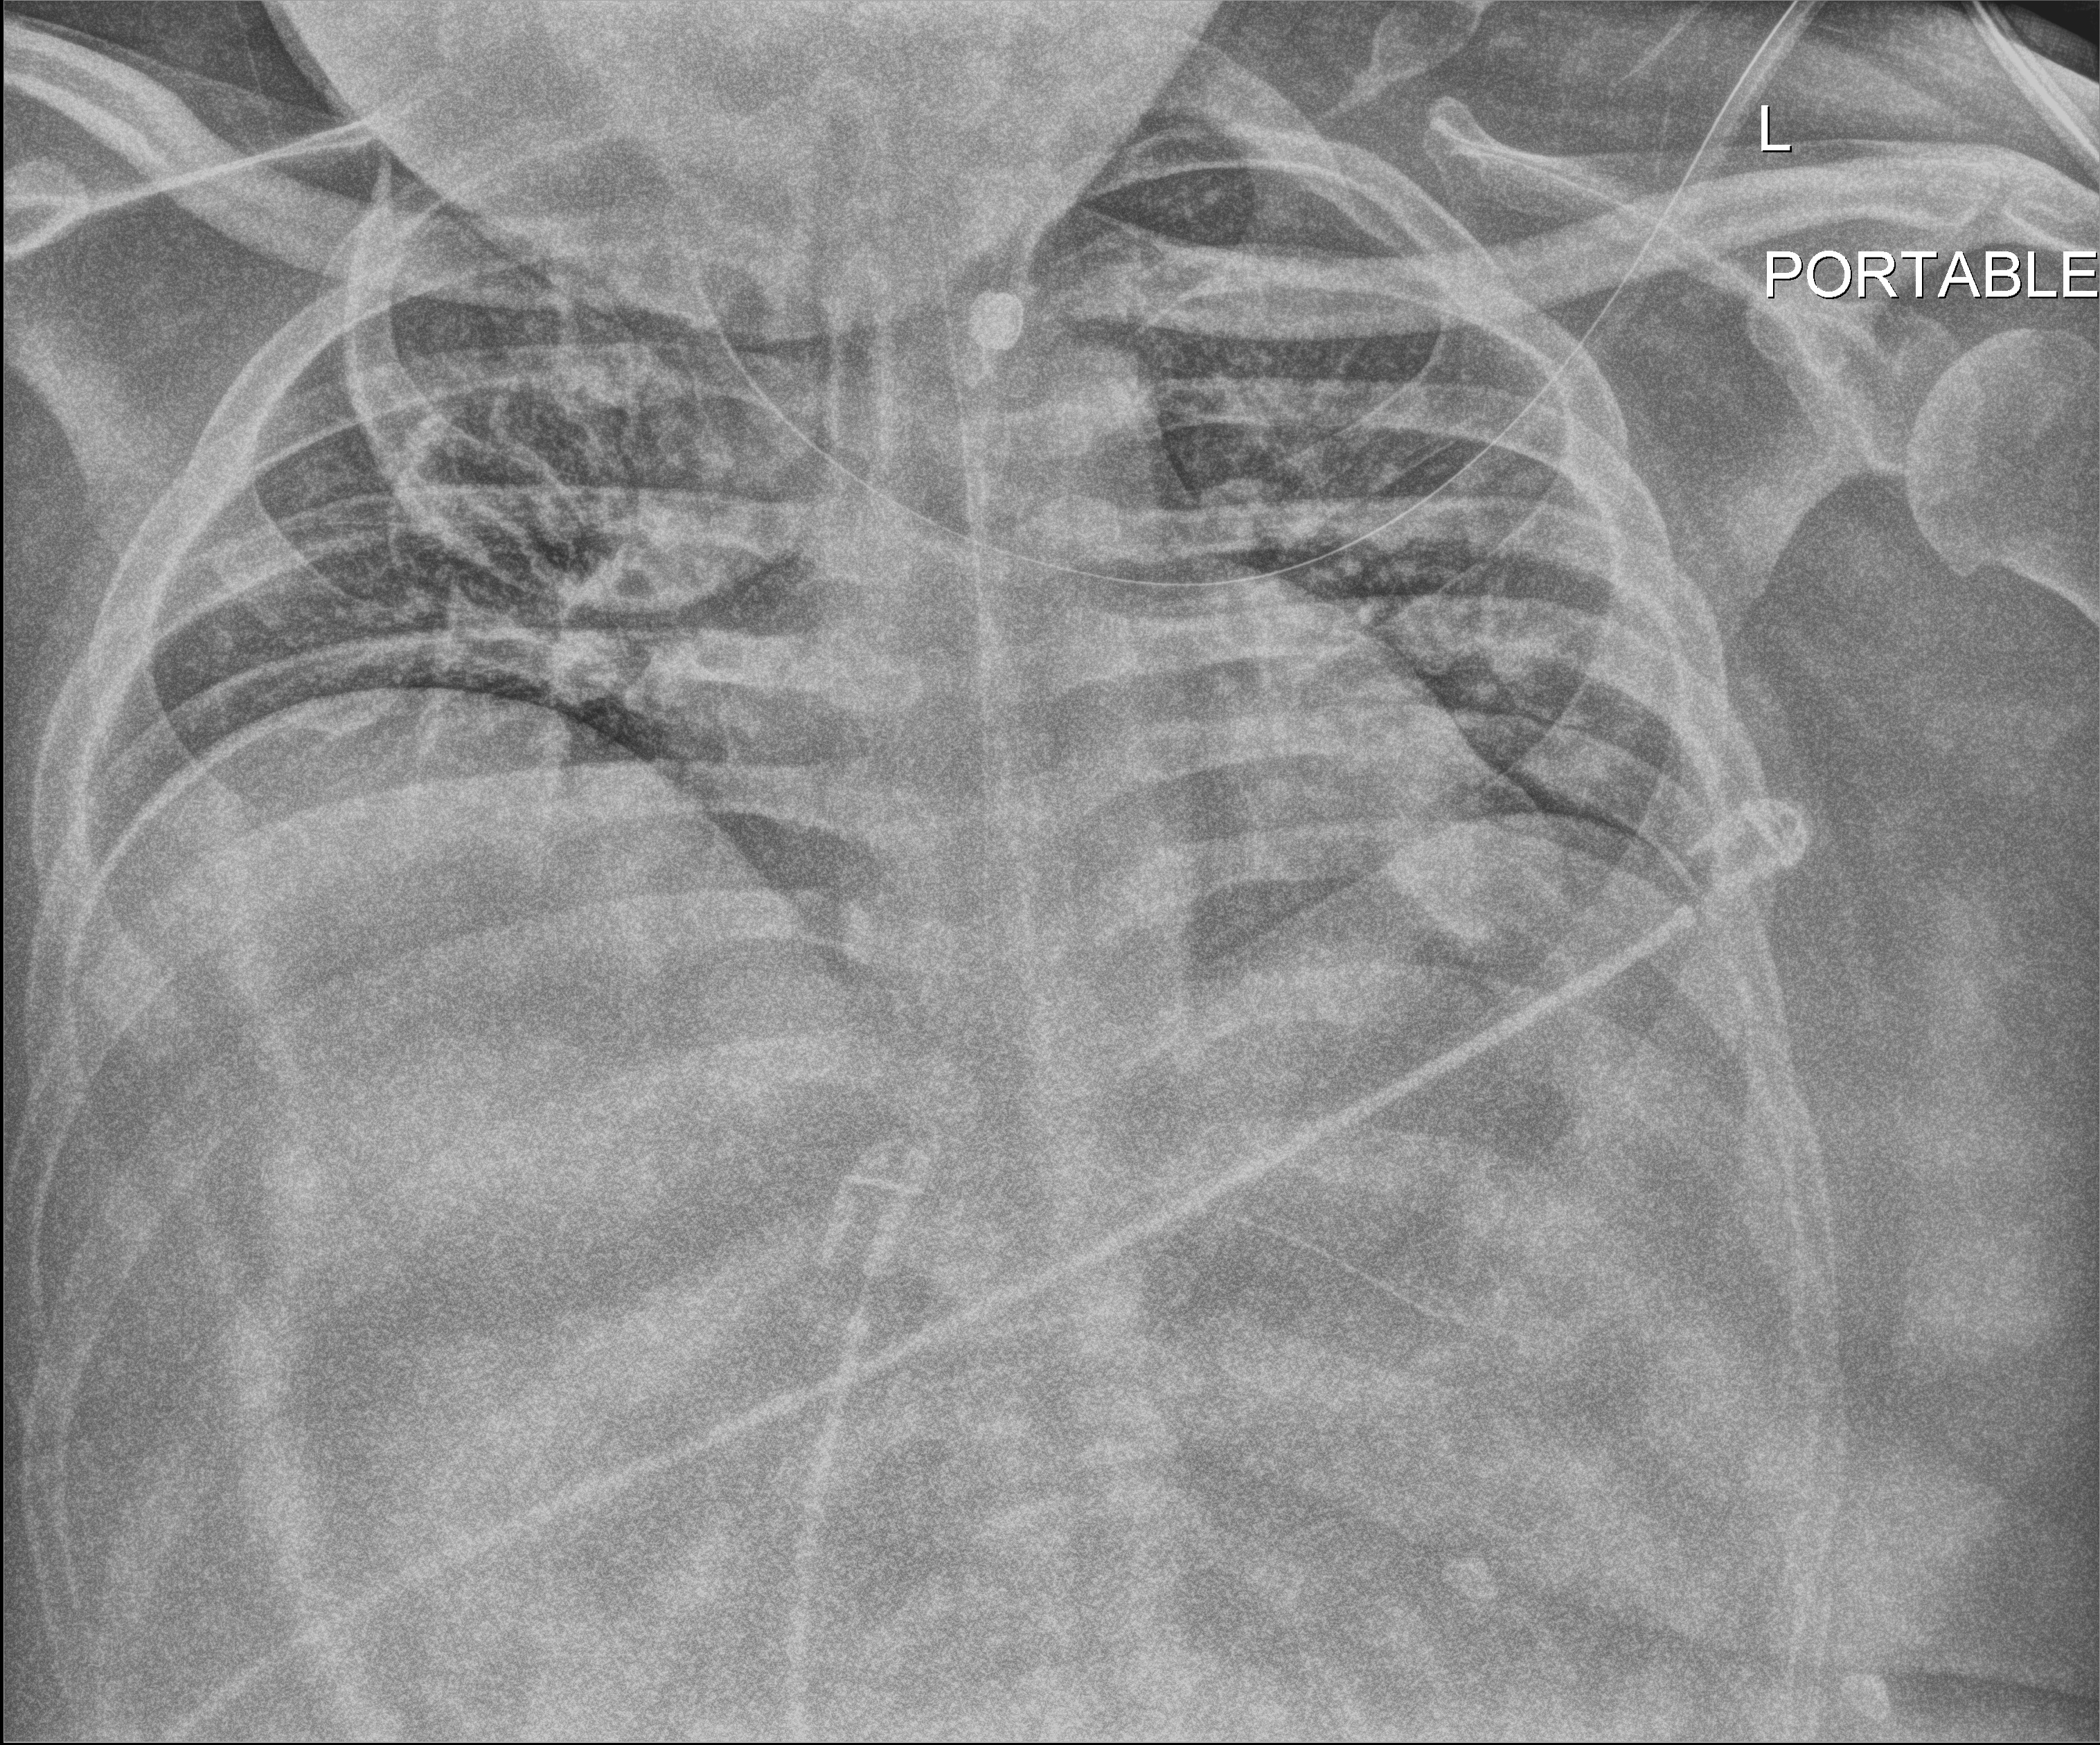
Chest X-ray (portable). Male patient hospitalised with COVID-19, age 18–59 years.
Admission-level facts for this patient (not findings on this image; timing relative to this image not recorded):
- length of hospital stay: 69 days
- mechanically ventilated during this hospital stay: yes
- chronic kidney disease (admission record): no